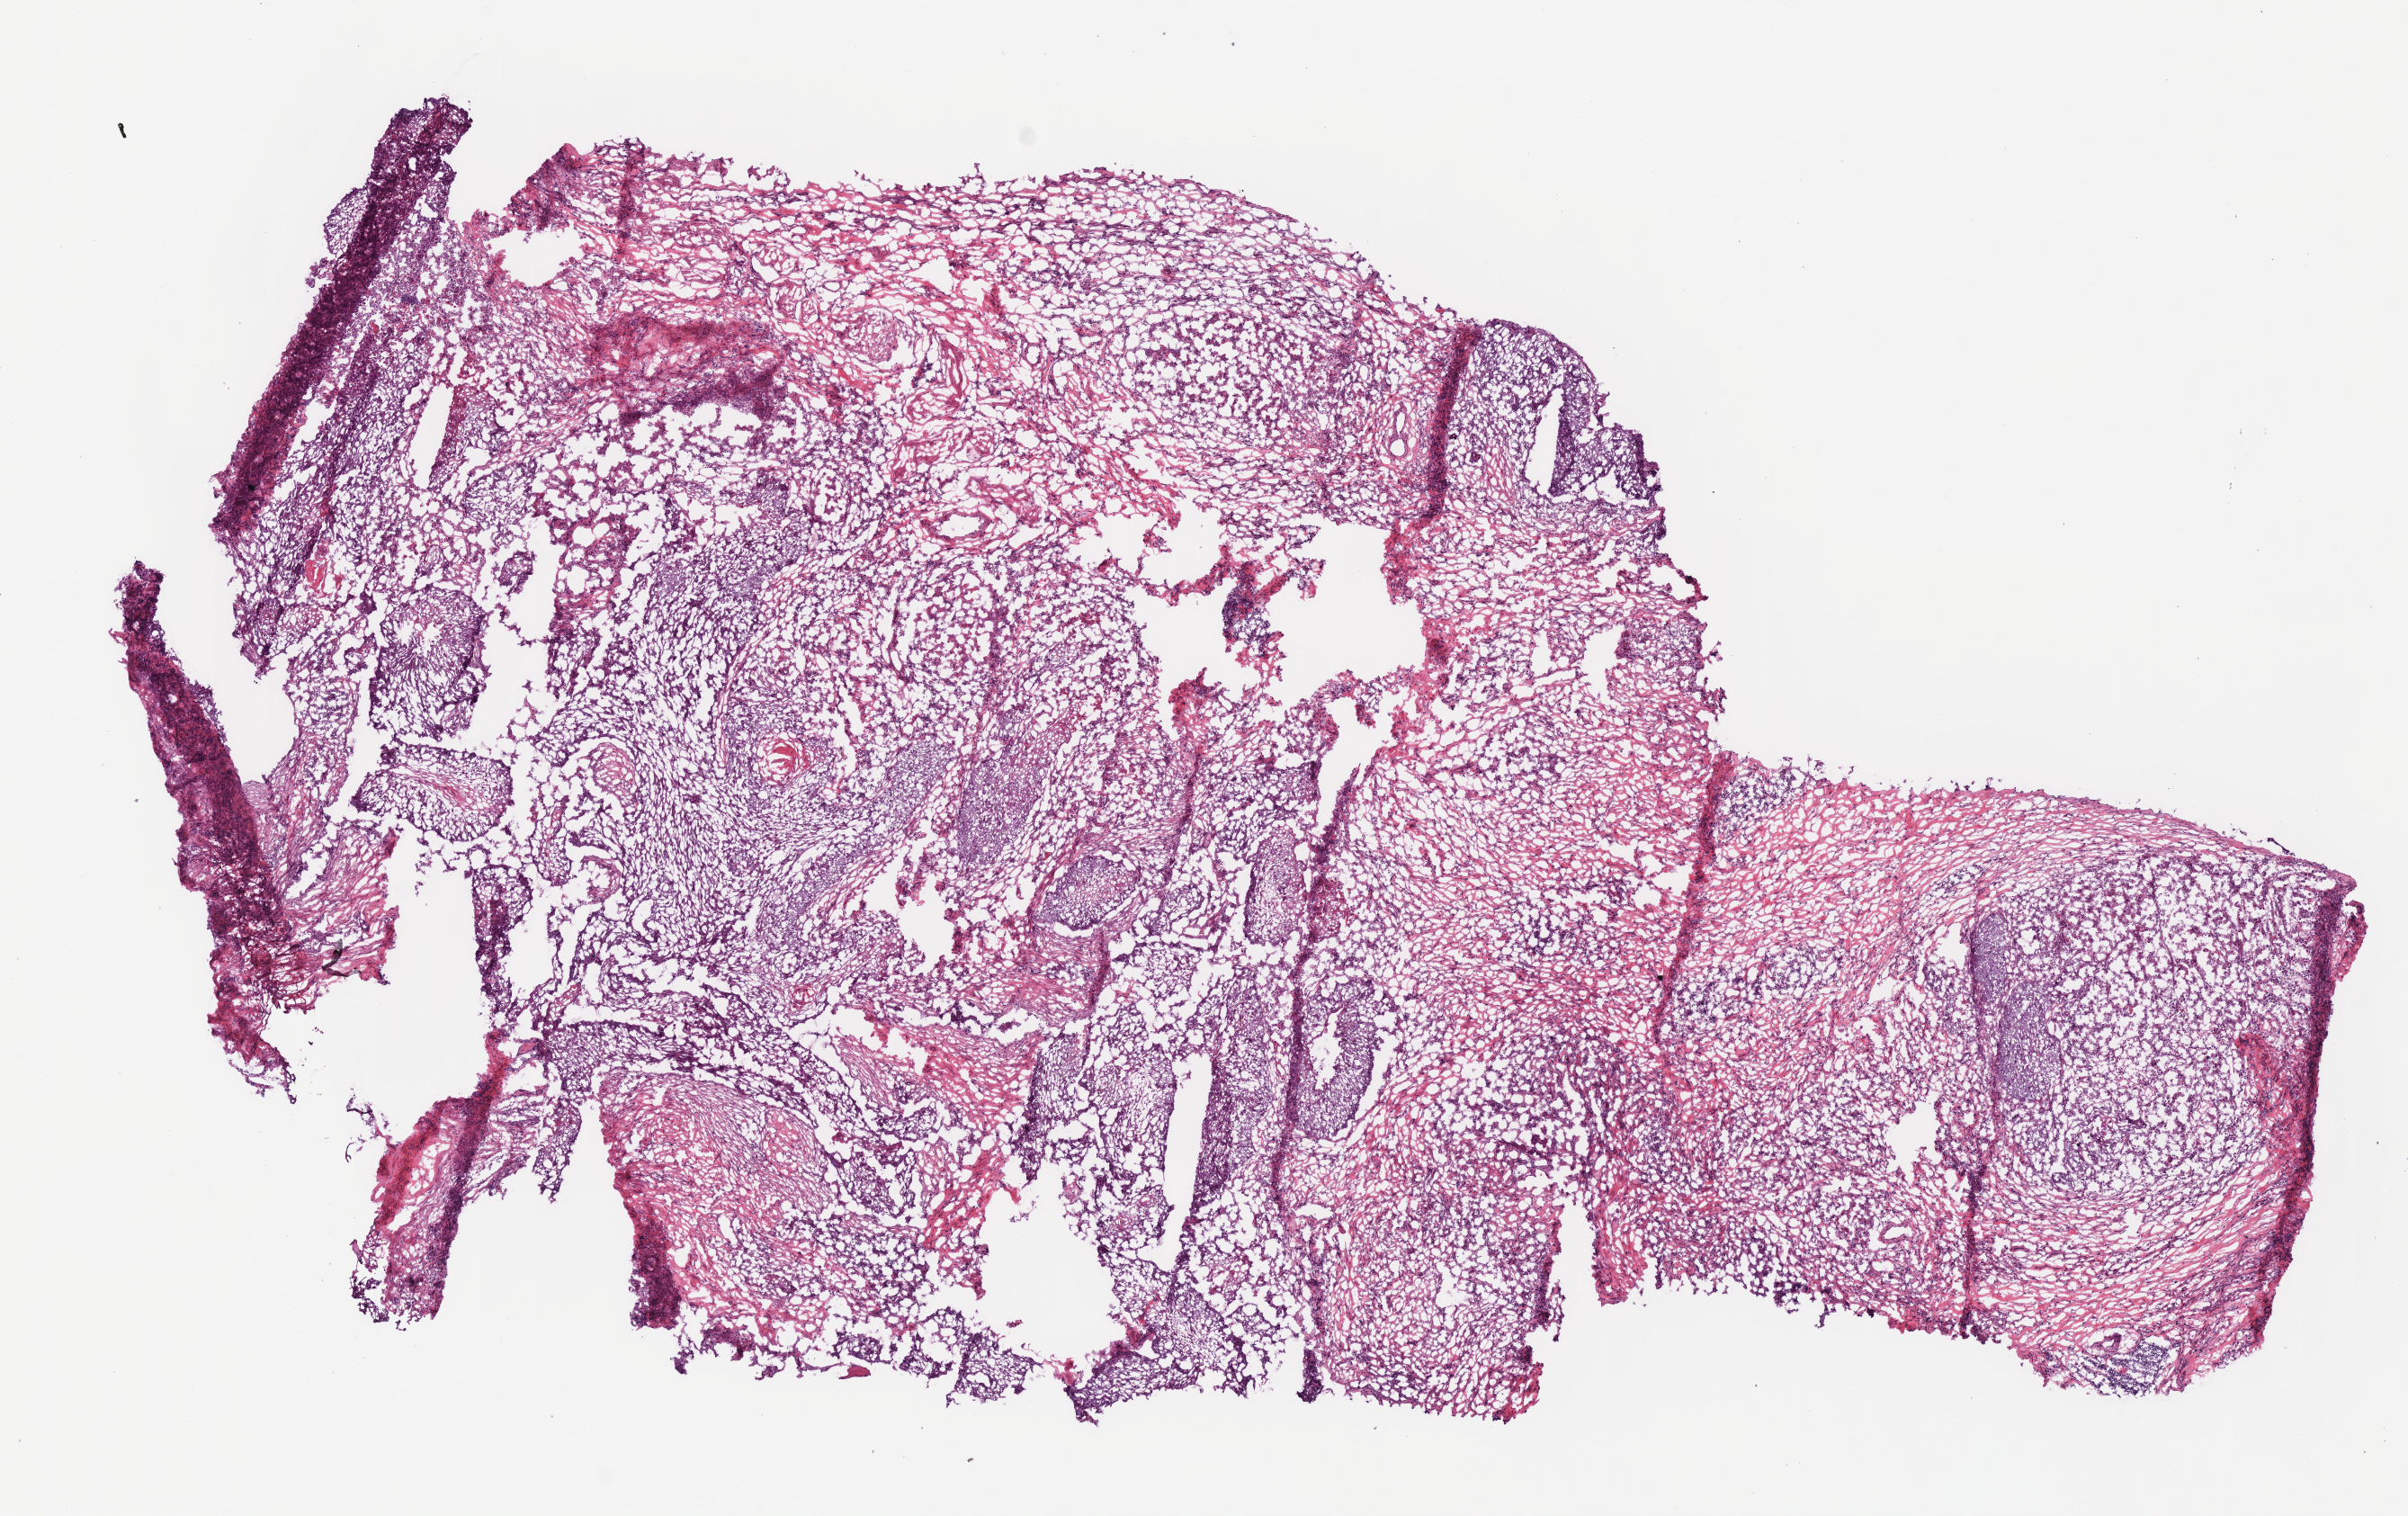
H&E-stained whole-slide image, shown as a low-resolution overview of the whole scanned area (about 10.5 x 6.6 mm, slide scanned at 40x); frozen section; primary tumour sample from the head and neck. Patient: female, age at initial diagnosis 60 years. Composition of this section per pathologist review: tumour cells 60%, tumour nuclei 60%.
Pathologic diagnosis: Squamous cell carcinoma, NOS (larynx, NOS).